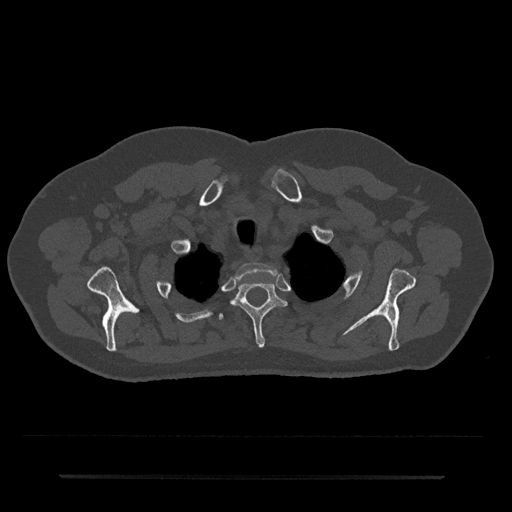
CT including the spine, one axial slice; slice 607 of 797 in the series (ordered by position); 120 kVp; bone window (W 1800 / L 400 HU); 0.5 mm slice thickness; 512 × 512 image matrix, field of view 437 × 437 mm. Male patient, age 69 years. Case-level facts recorded for this patient, not image findings: primary cancer: prostate.
Structures marked on this image (semi-automatically segmented with operator editing):
- T1 vertebra: bounding box <235,263,279,280> (left, top, right, bottom; pixels)
- T2 vertebra: <231,282,287,347>
- T3 vertebra: <219,313,223,320>